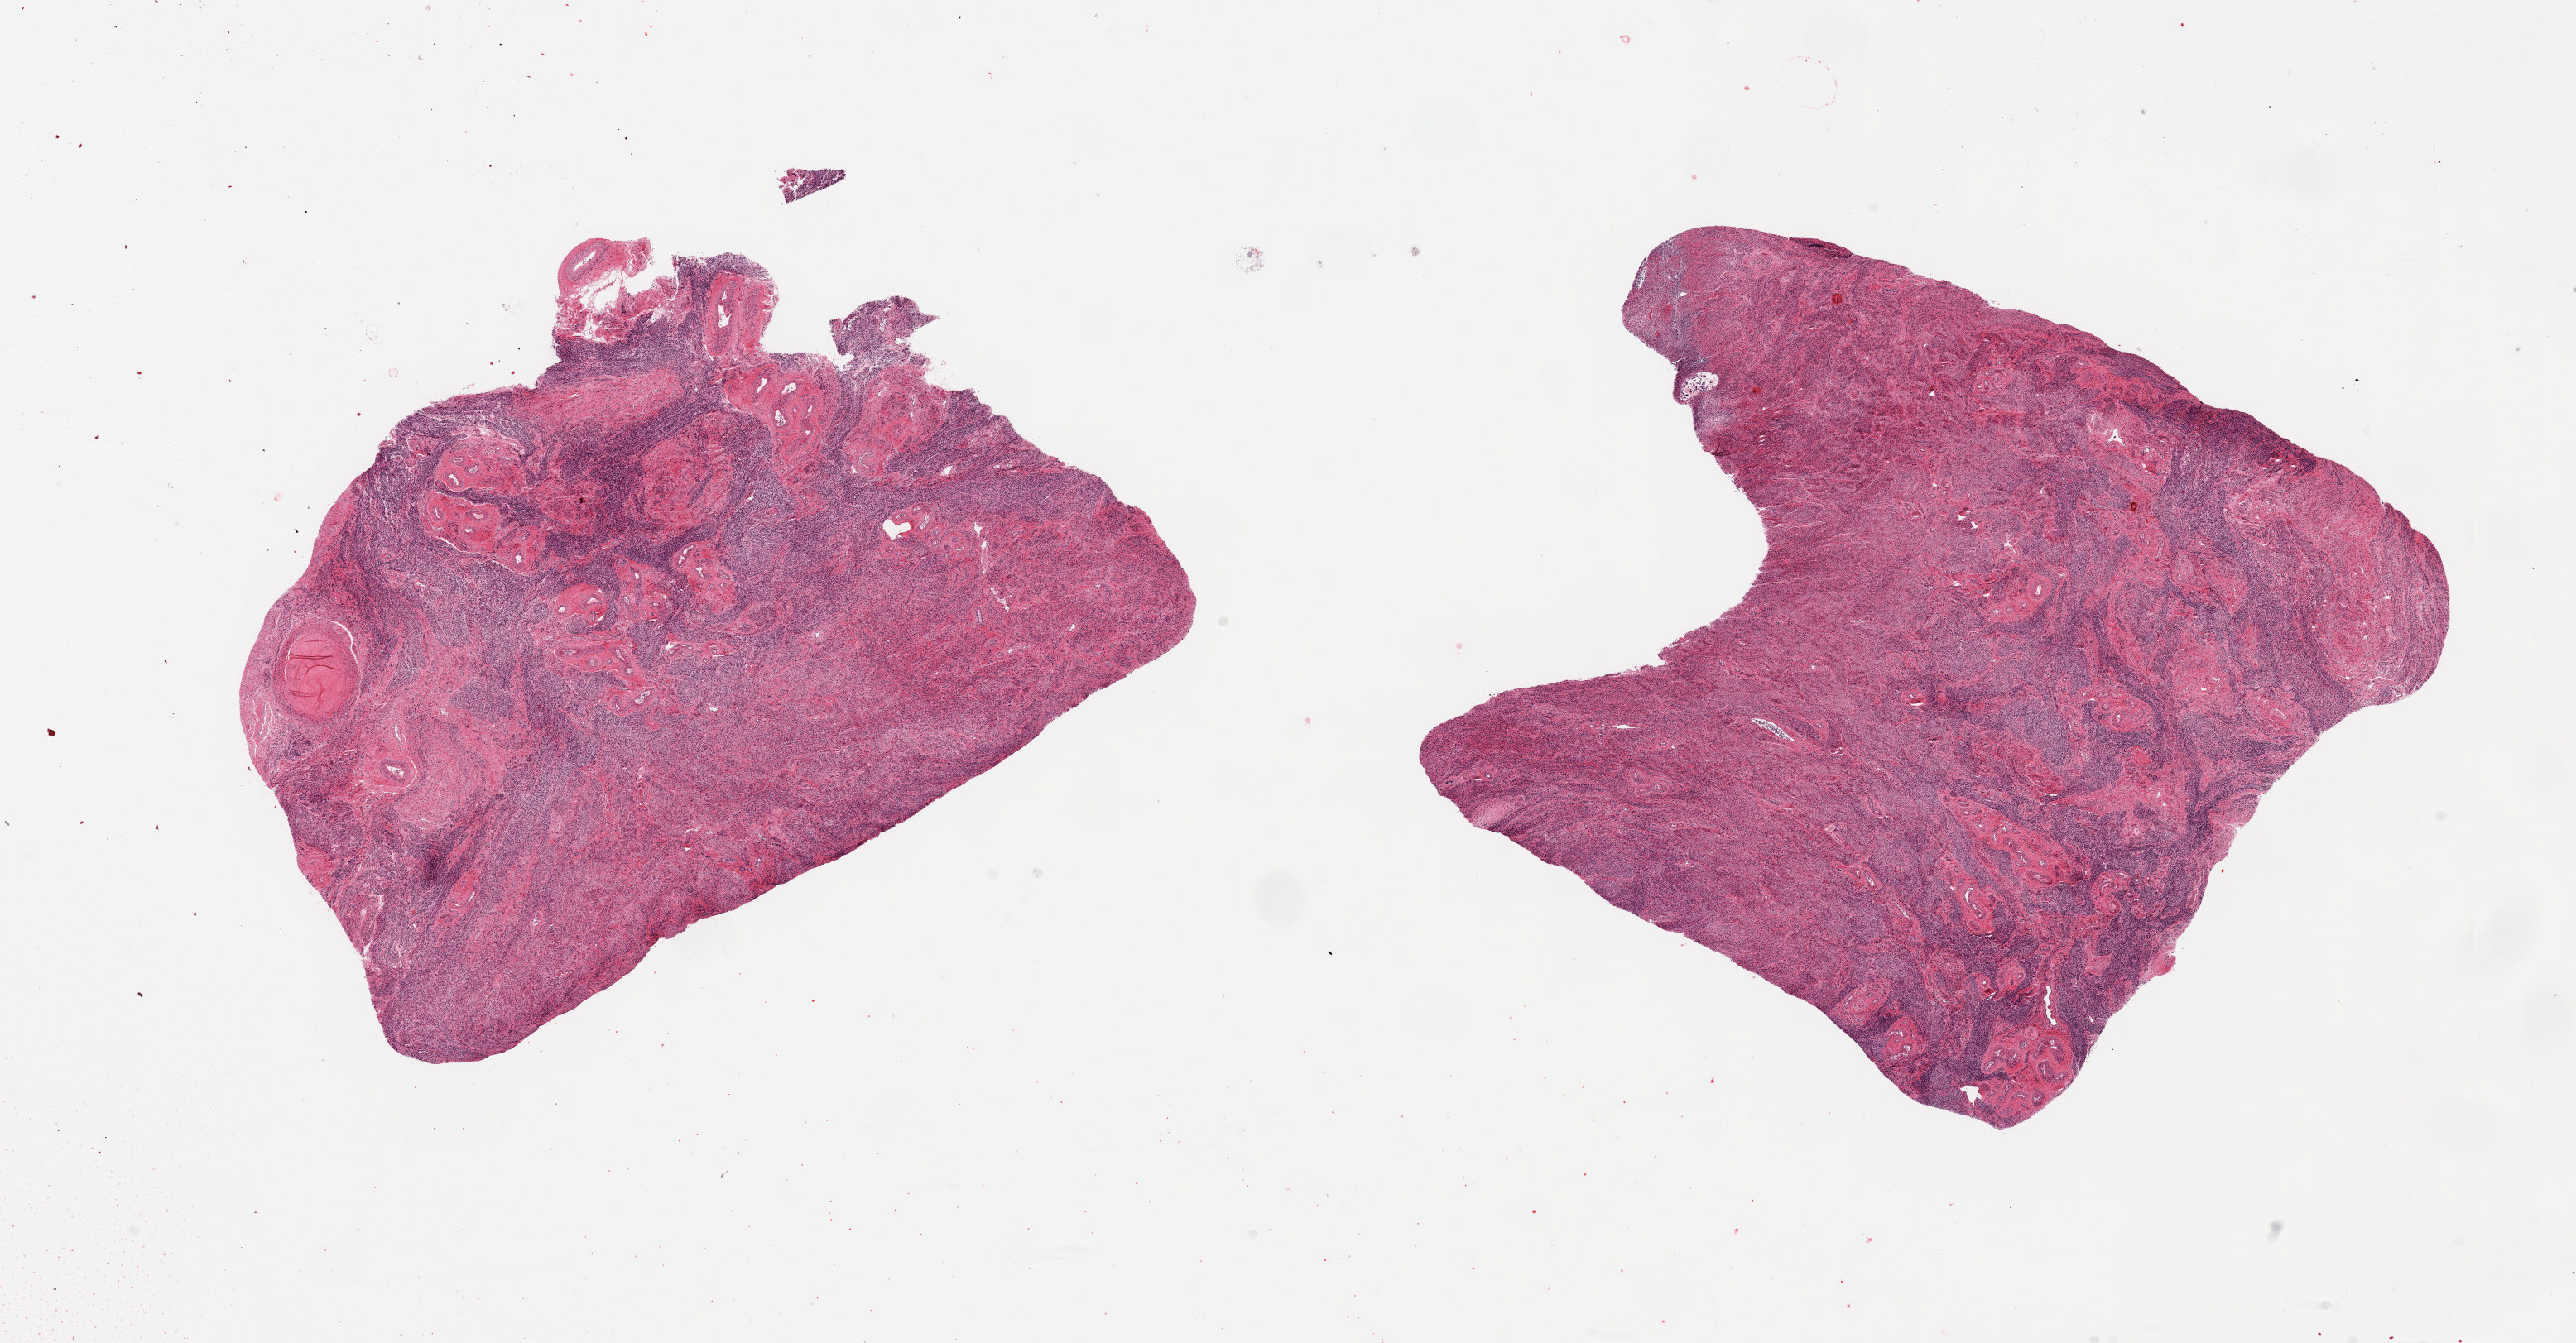
Digitized haematoxylin and eosin-stained section, brightfield — a low-resolution overview of the entire scanned area, about 24.6 x 12.8 mm (slide scanned at 20x), PAXgene-fixed paraffin-embedded (PFPE) section, target tissue: uterus, tissue donor sample. Donor: female.
Pathologist's review note for this sample: 2 pieces; little, if any, endometrium in these cuts.